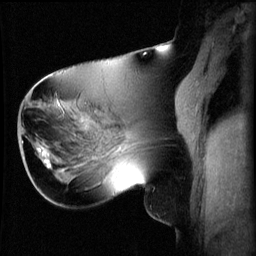
Breast MRI (dynamic contrast-enhanced), one sagittal slice. 3 images stored at this slice position (order not interpretable as contrast timing). 1.5 T. TE 4.2 ms, TR 8.2 ms. 256 × 256 image matrix, field of view 220 × 220 mm. Female patient, age 62 years.
Annotated regions visible in this slice (semi-automatically segmented with operator editing):
- analysis volume of interest (the breast-tissue region the enhancement analysis was run in; not a lesion): bounding box (x1, y1, x2, y2) in pixels: (32, 128, 59, 165)
- tumour enhancement mask (voxels above the 70 % enhancement threshold inside the analysis volume of interest): (38, 148, 51, 165)